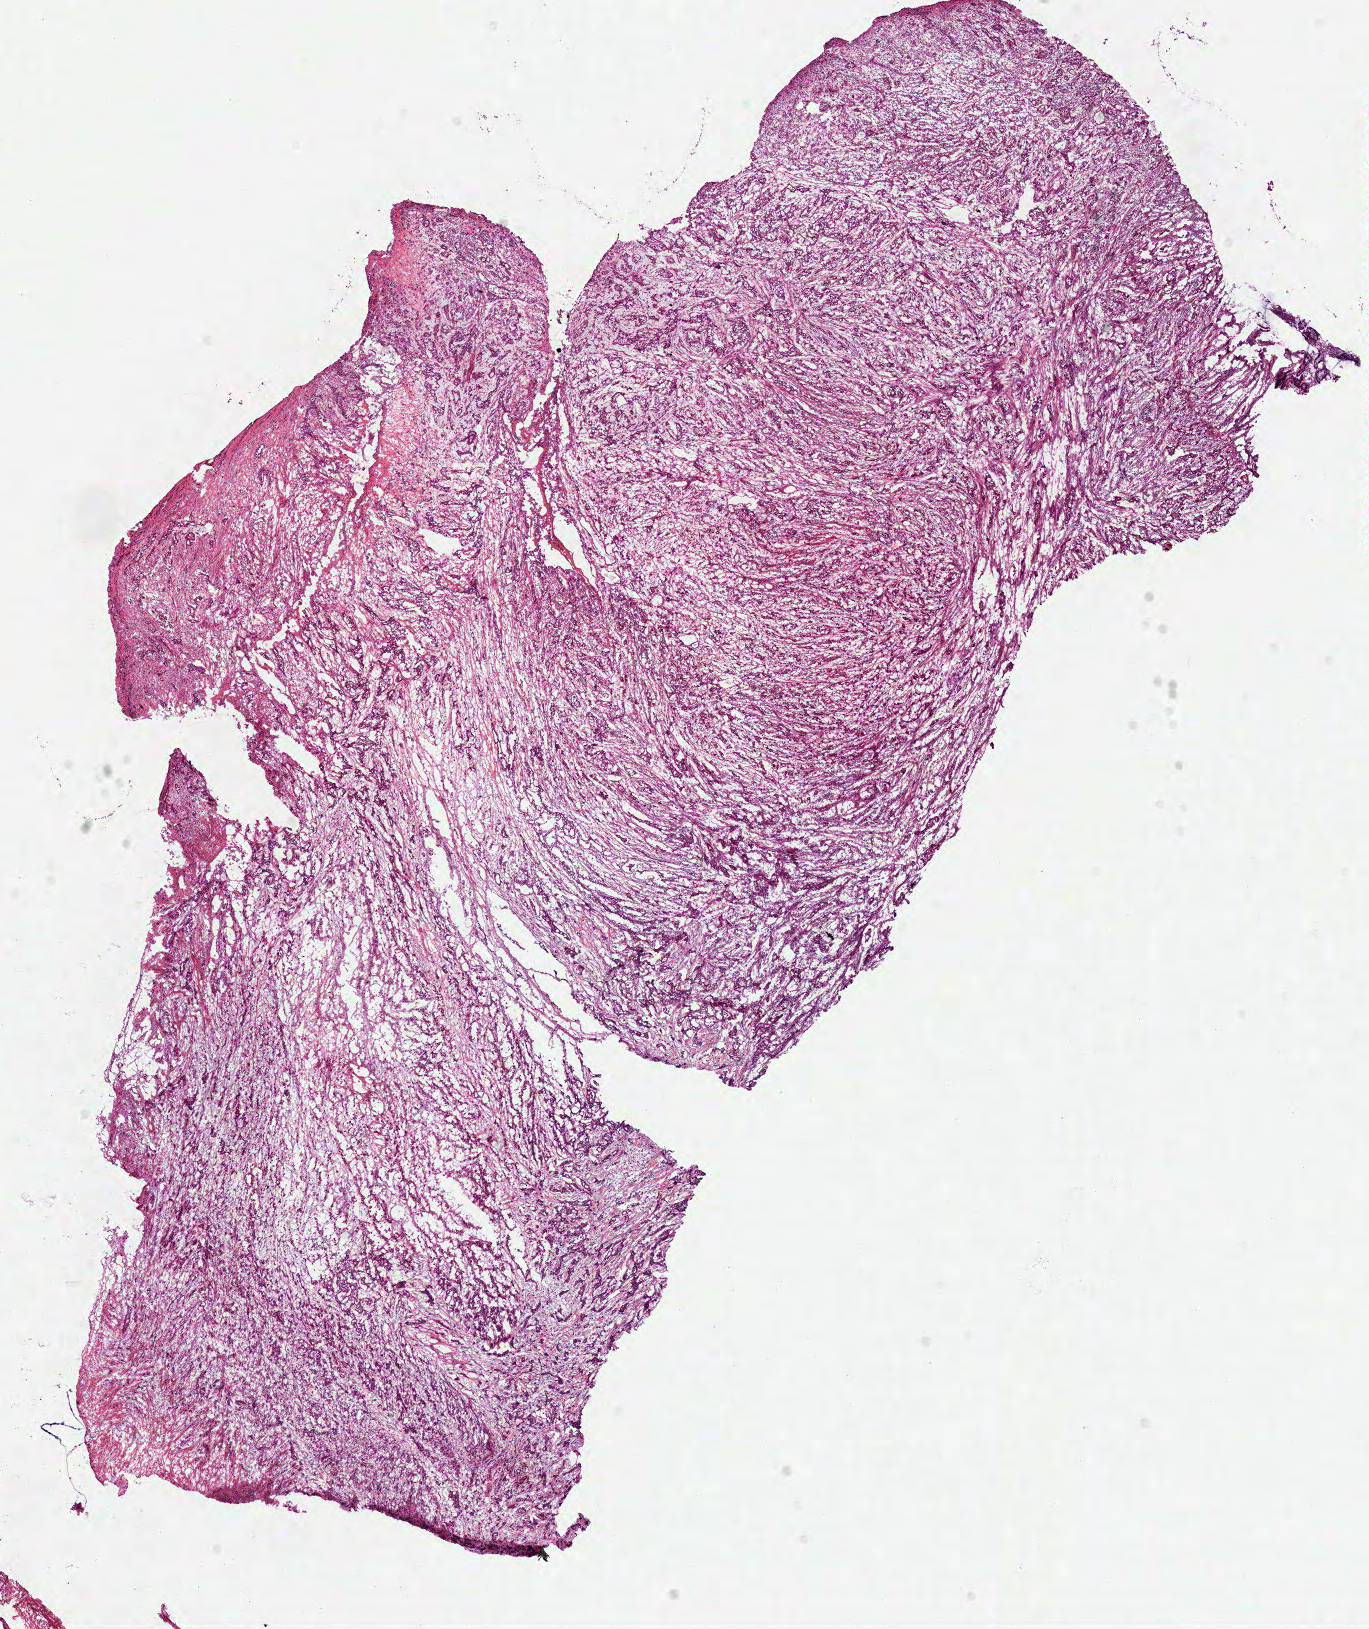
H&E whole-slide image, whole scanned area (about 10.8 x 12.8 mm, acquisition: 40x scan) shown as a low-resolution overview. Frozen section. Primary tumour sample from the colon. Patient: male, age at initial diagnosis 69 years. Slide review estimates, as recorded: tumour cells 80%, tumour nuclei 80%, normal cells 0%, stromal cells 20%, necrosis 0%.
* histologic diagnosis: Adenocarcinoma, NOS (sigmoid colon)
* lymph nodes positive (case pathology): 5 of 19 examined
* AJCC pathologic stage: IV